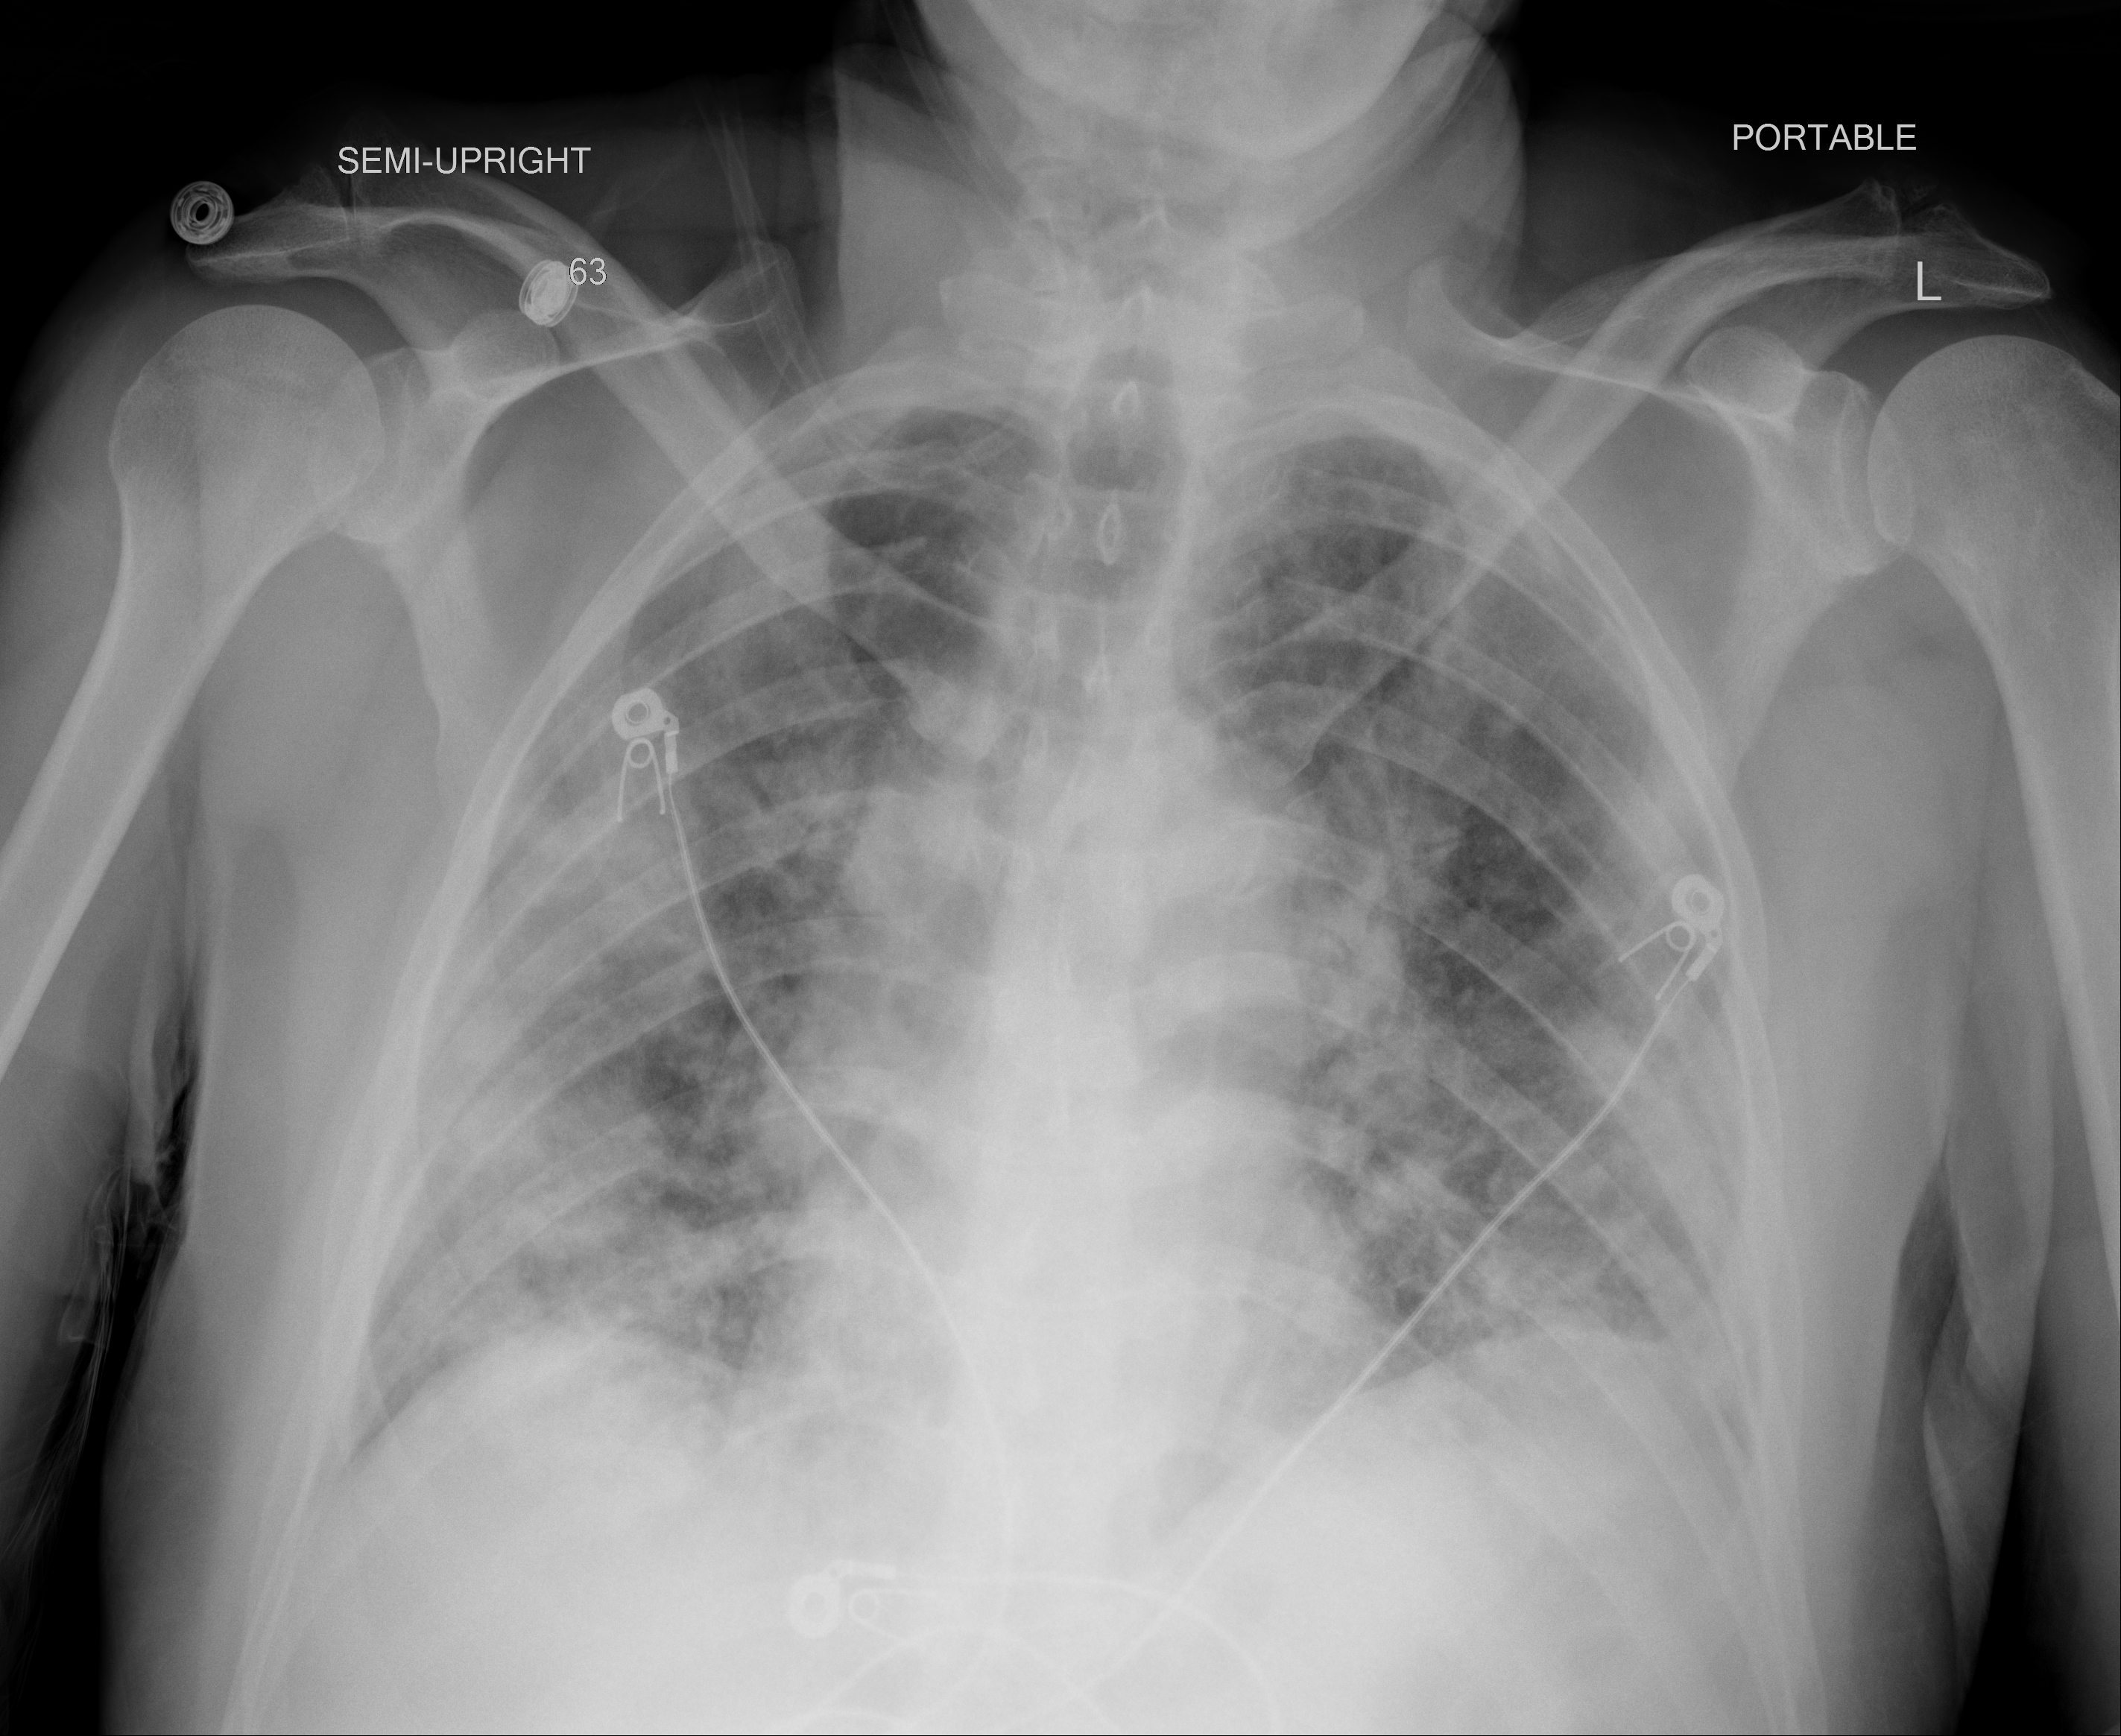
Portable chest radiograph, AP projection. Male patient, age 66 years; imaged 5 days after the COVID-19 diagnosis.
Radiologist's key findings for this exam: Significant interval worsening in bilateral mid and lower lung confluent peripheral airspace opacities.